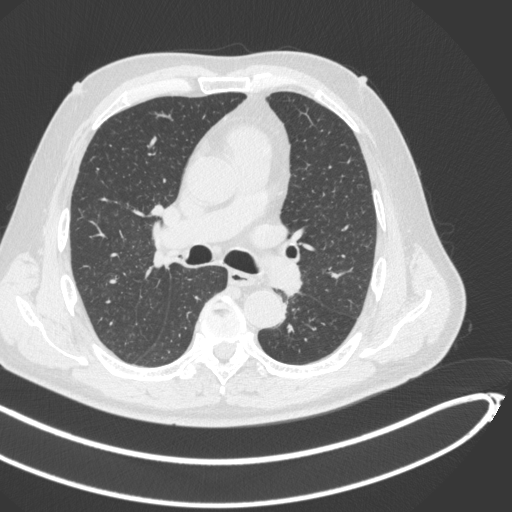
Chest CT, one axial slice. Slice 278 of 466 in the series (ordered by position). Reconstruction kernel B31f. Lung window (W 1500 / L -600 HU). 1 mm slice thickness. 512 × 512 image matrix. Patient: male, 64 years. From the clinical record (not read from this slice): clinical TNM (as recorded): T1c N0 M0; histopathological grade: G2.
Structures marked on this image (rectangle marked by the reading radiologist):
- lung tumour (recorded histology: squamous cell carcinoma): box from (x=261, y=251) to (x=305, y=300) px